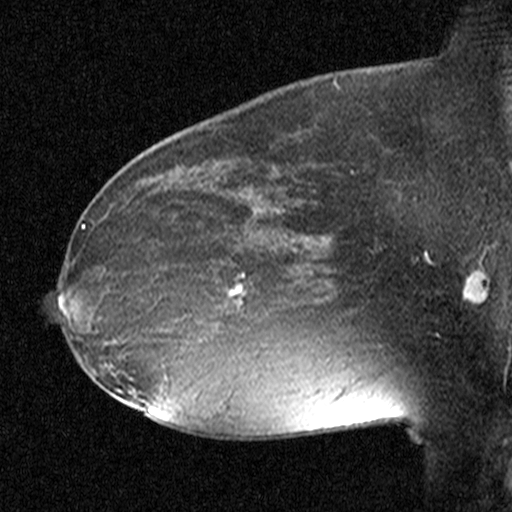
Breast MRI (dynamic contrast-enhanced), one sagittal slice. Position 28 of 44 along the scan axis. Dynamic contrast-enhanced study with each time point stored as its own series, time point 2 of 3 at this slice position (early post-contrast, ordered by acquisition time). 1.5 T. TE 4.5 ms, TR 11 ms. 512 × 512 image matrix, field of view 200 × 200 mm. Patient: female, 38 years. Case-level facts recorded for this patient, not image findings: setting: breast cancer imaged before/during neoadjuvant chemotherapy; receptor status: HR-positive, HER2-negative.
Annotated regions visible in this slice (semi-automatically segmented with operator editing):
- analysis volume of interest (the breast-tissue region the enhancement analysis was run in; not a lesion): bounding box <182,232,291,349> (left, top, right, bottom; pixels)
- tumour enhancement mask (voxels above the 90 % enhancement threshold inside the analysis volume of interest): <228,234,267,306>